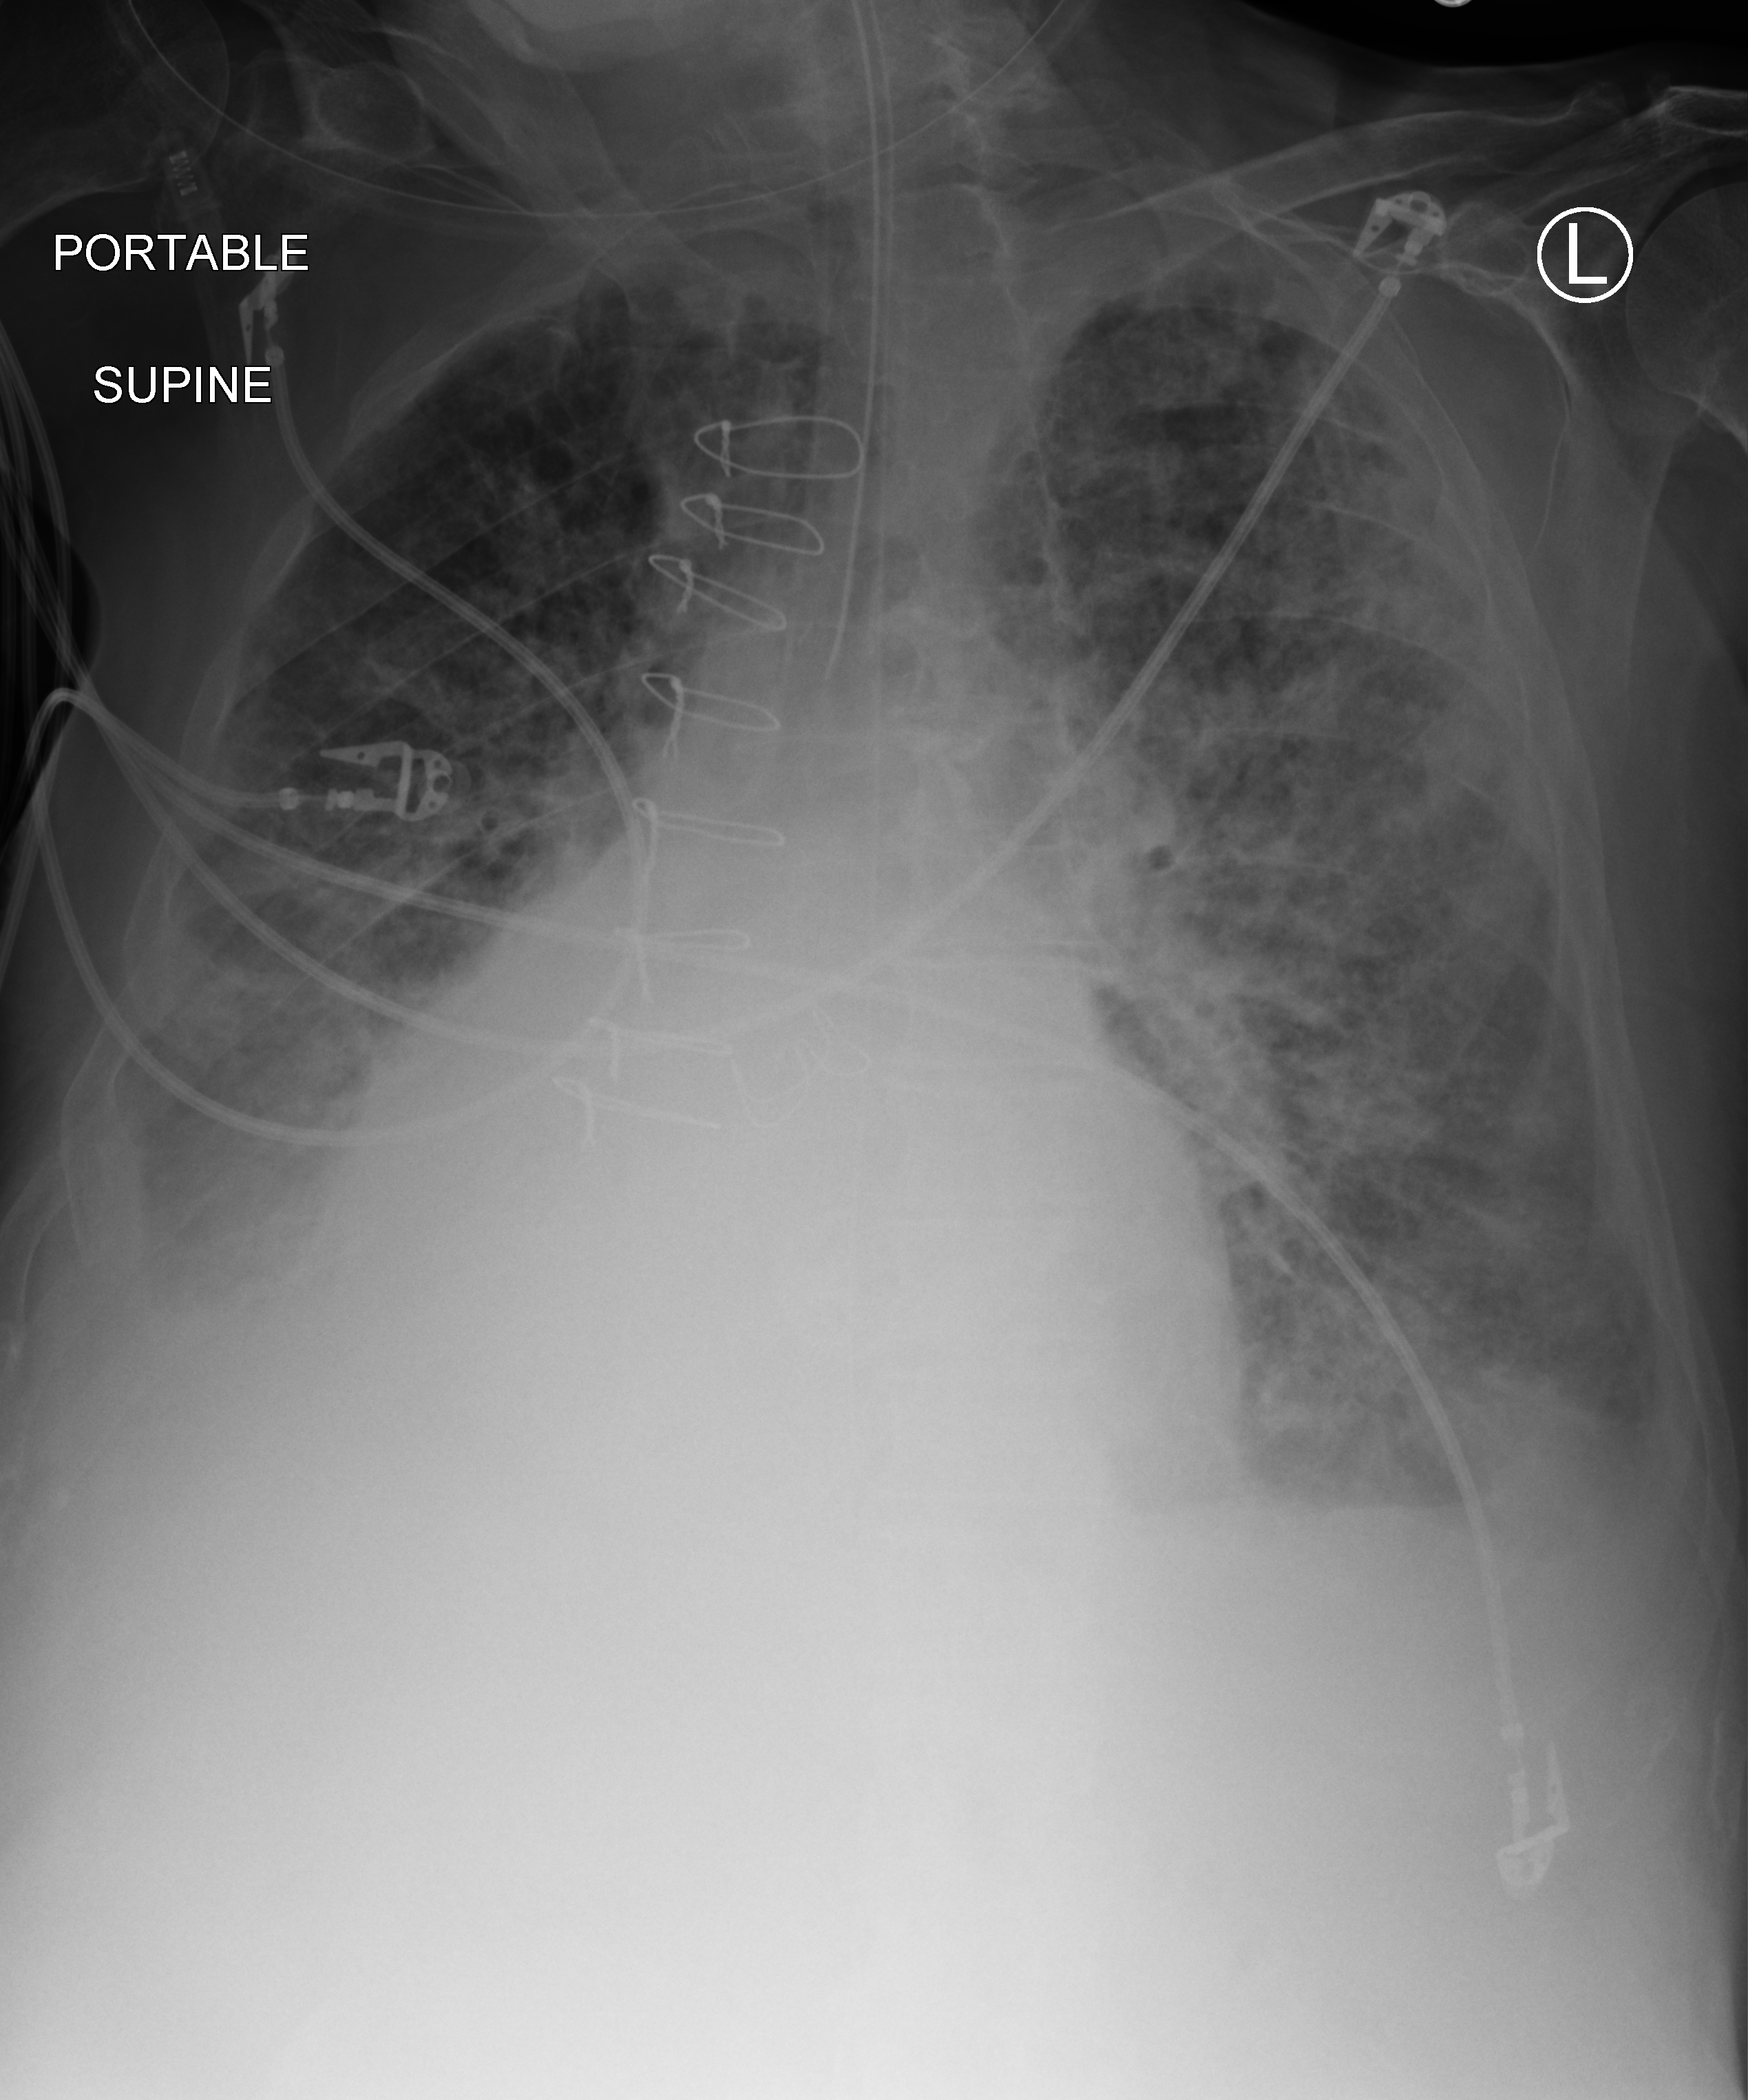
Portable chest radiograph; anteroposterior (AP) projection. Patient hospitalised with COVID-19; male, aged 75–90 years.
Admission-level facts for this patient (not findings on this image; timing relative to this image not recorded):
- mechanically ventilated during this hospital stay: yes
- admitted to intensive care during this hospital stay: yes